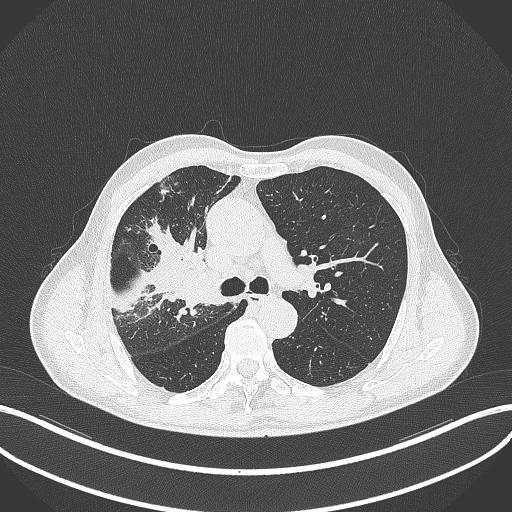
Chest CT, one axial slice; slice 319 of 490 in the series (ordered by position); 120 kVp; lung window (W 1500 / L -600 HU); 1 mm slice thickness; 512 × 512 image matrix. Male patient, age 69 years. Case-level facts recorded for this patient, not image findings: clinical TNM (as recorded): T2a N0 M0.
Annotated regions visible in this slice (bounding box drawn by a radiologist):
- lung tumour (recorded histology: adenocarcinoma): bounding box [x1, y1, x2, y2] px = [171, 256, 229, 311]